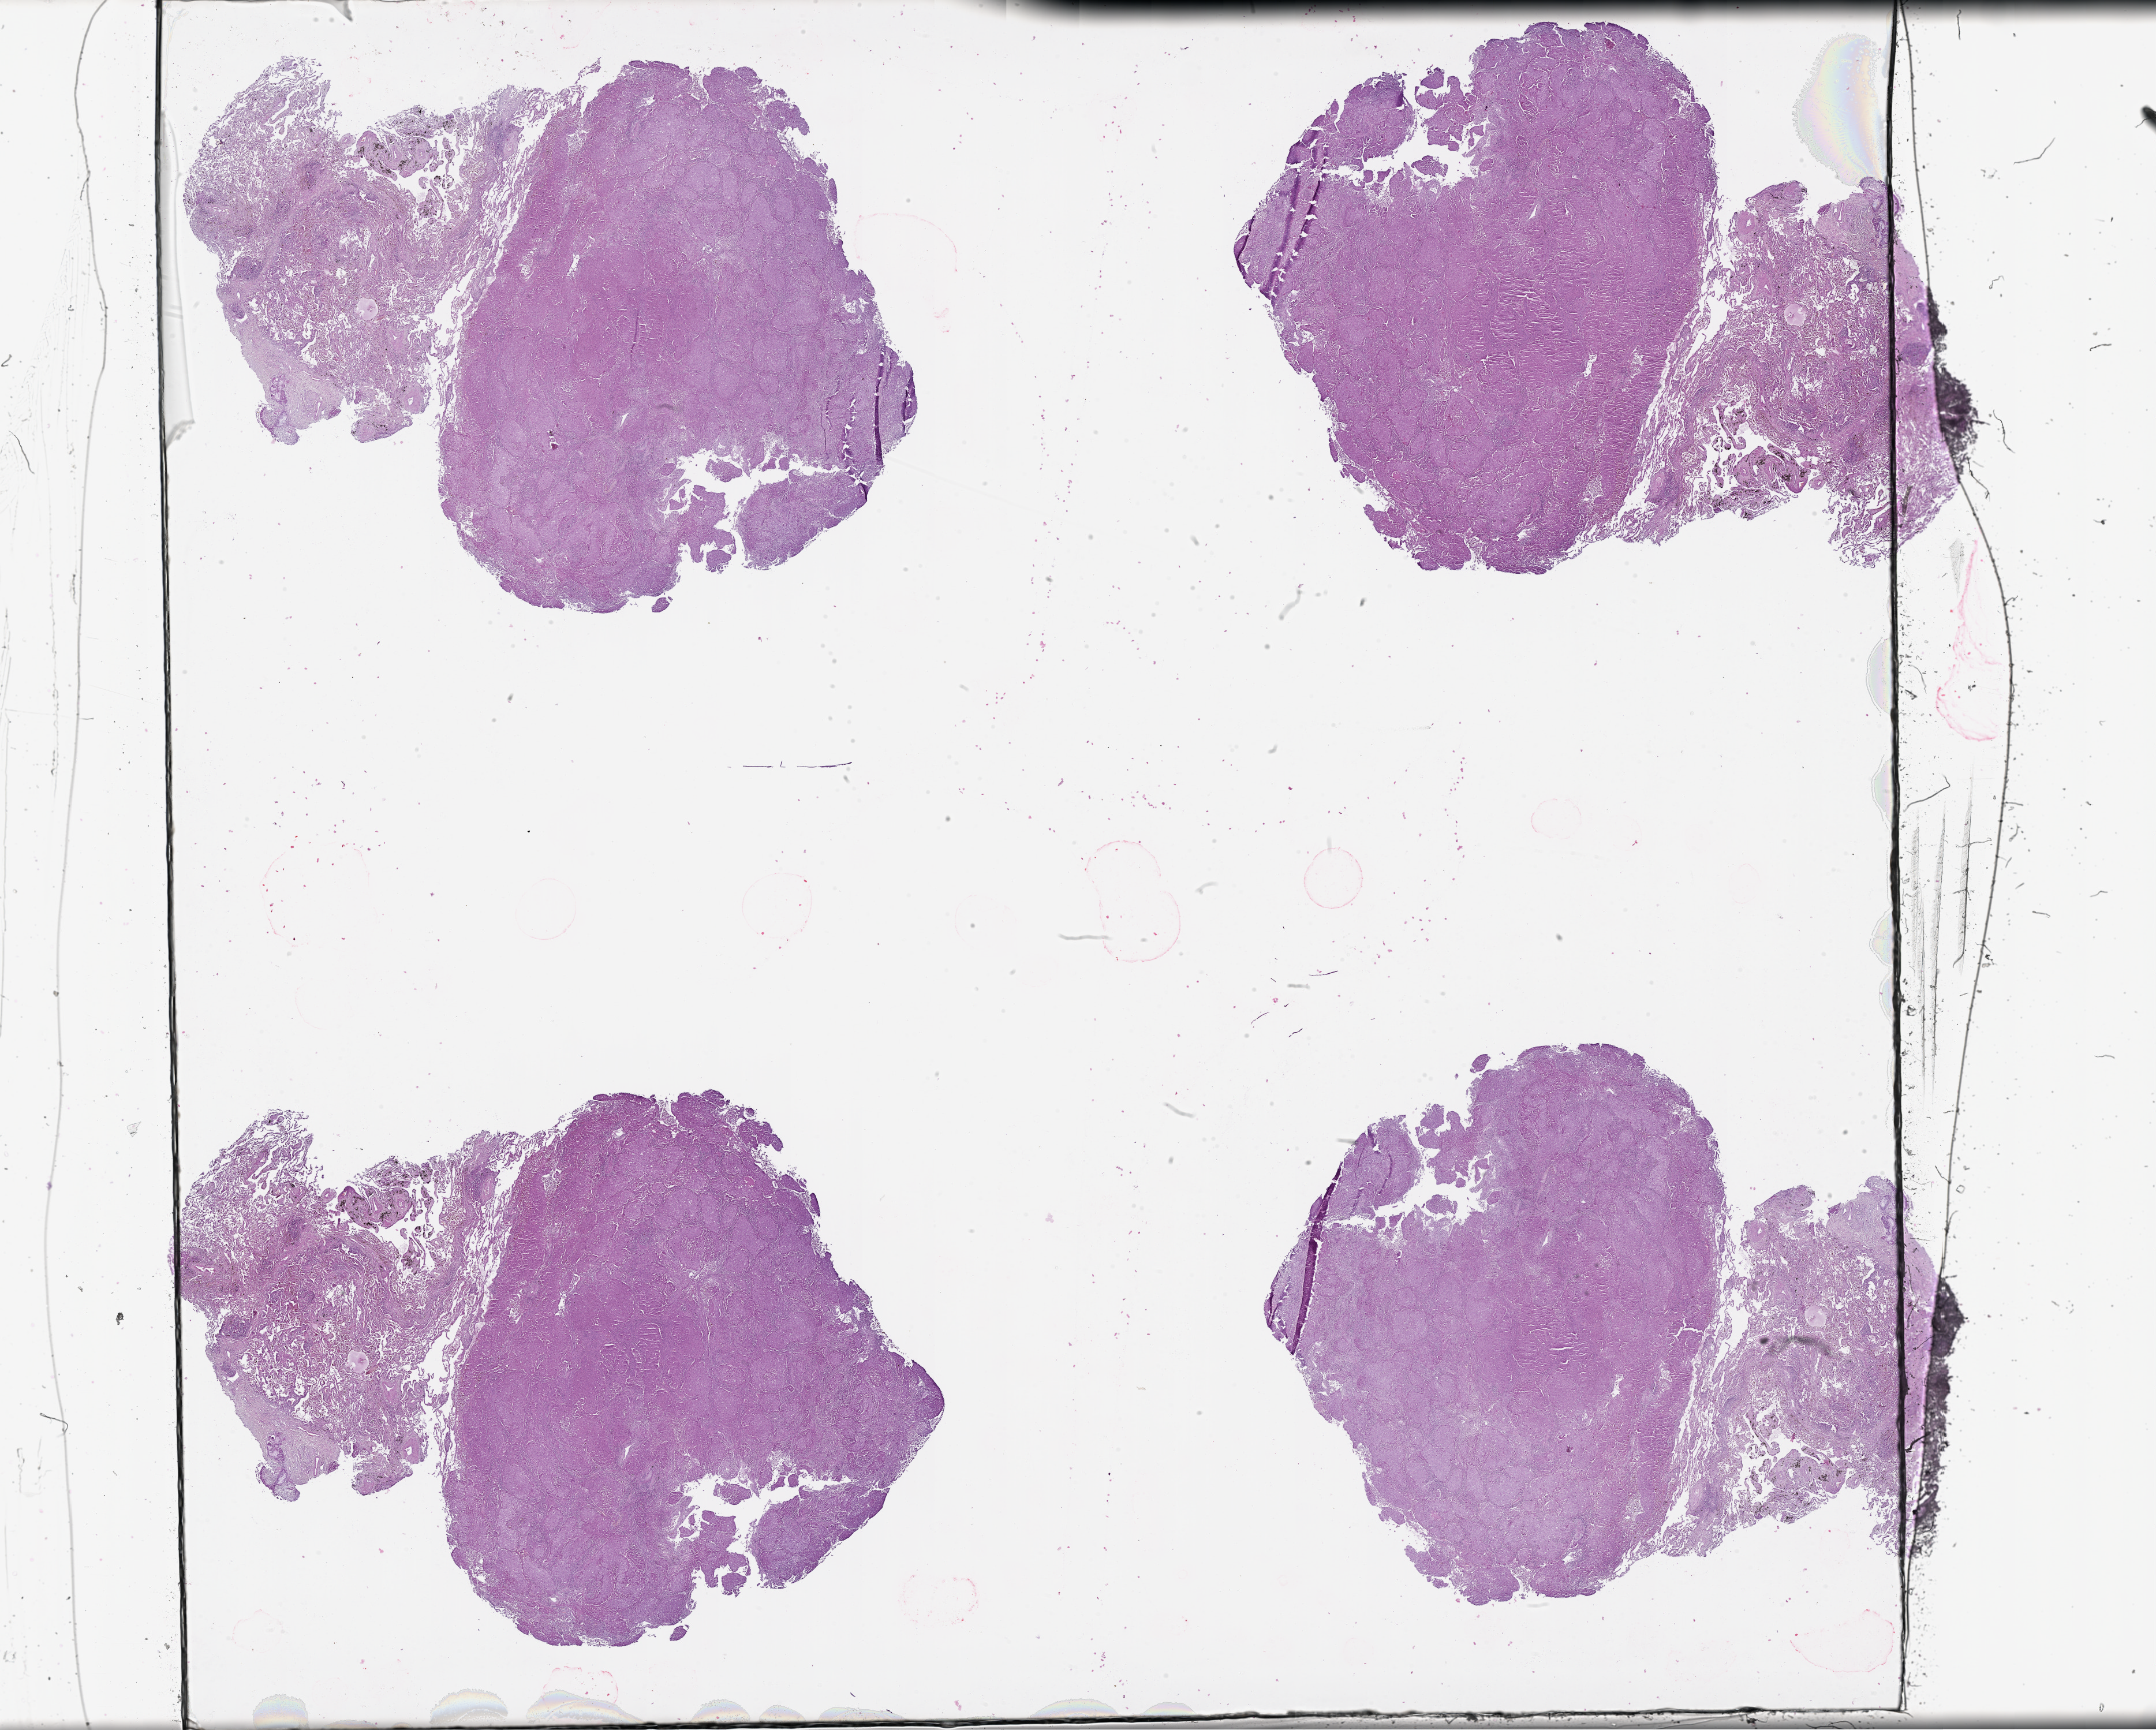
H&E whole-slide image, low-resolution overview of the scanned area, about 30.1 x 24.1 mm (from a 20x scan), lung, tumour tissue. Male, 61 y/o.
Patient diagnosis (cohort enrolment): squamous cell carcinoma (lung).